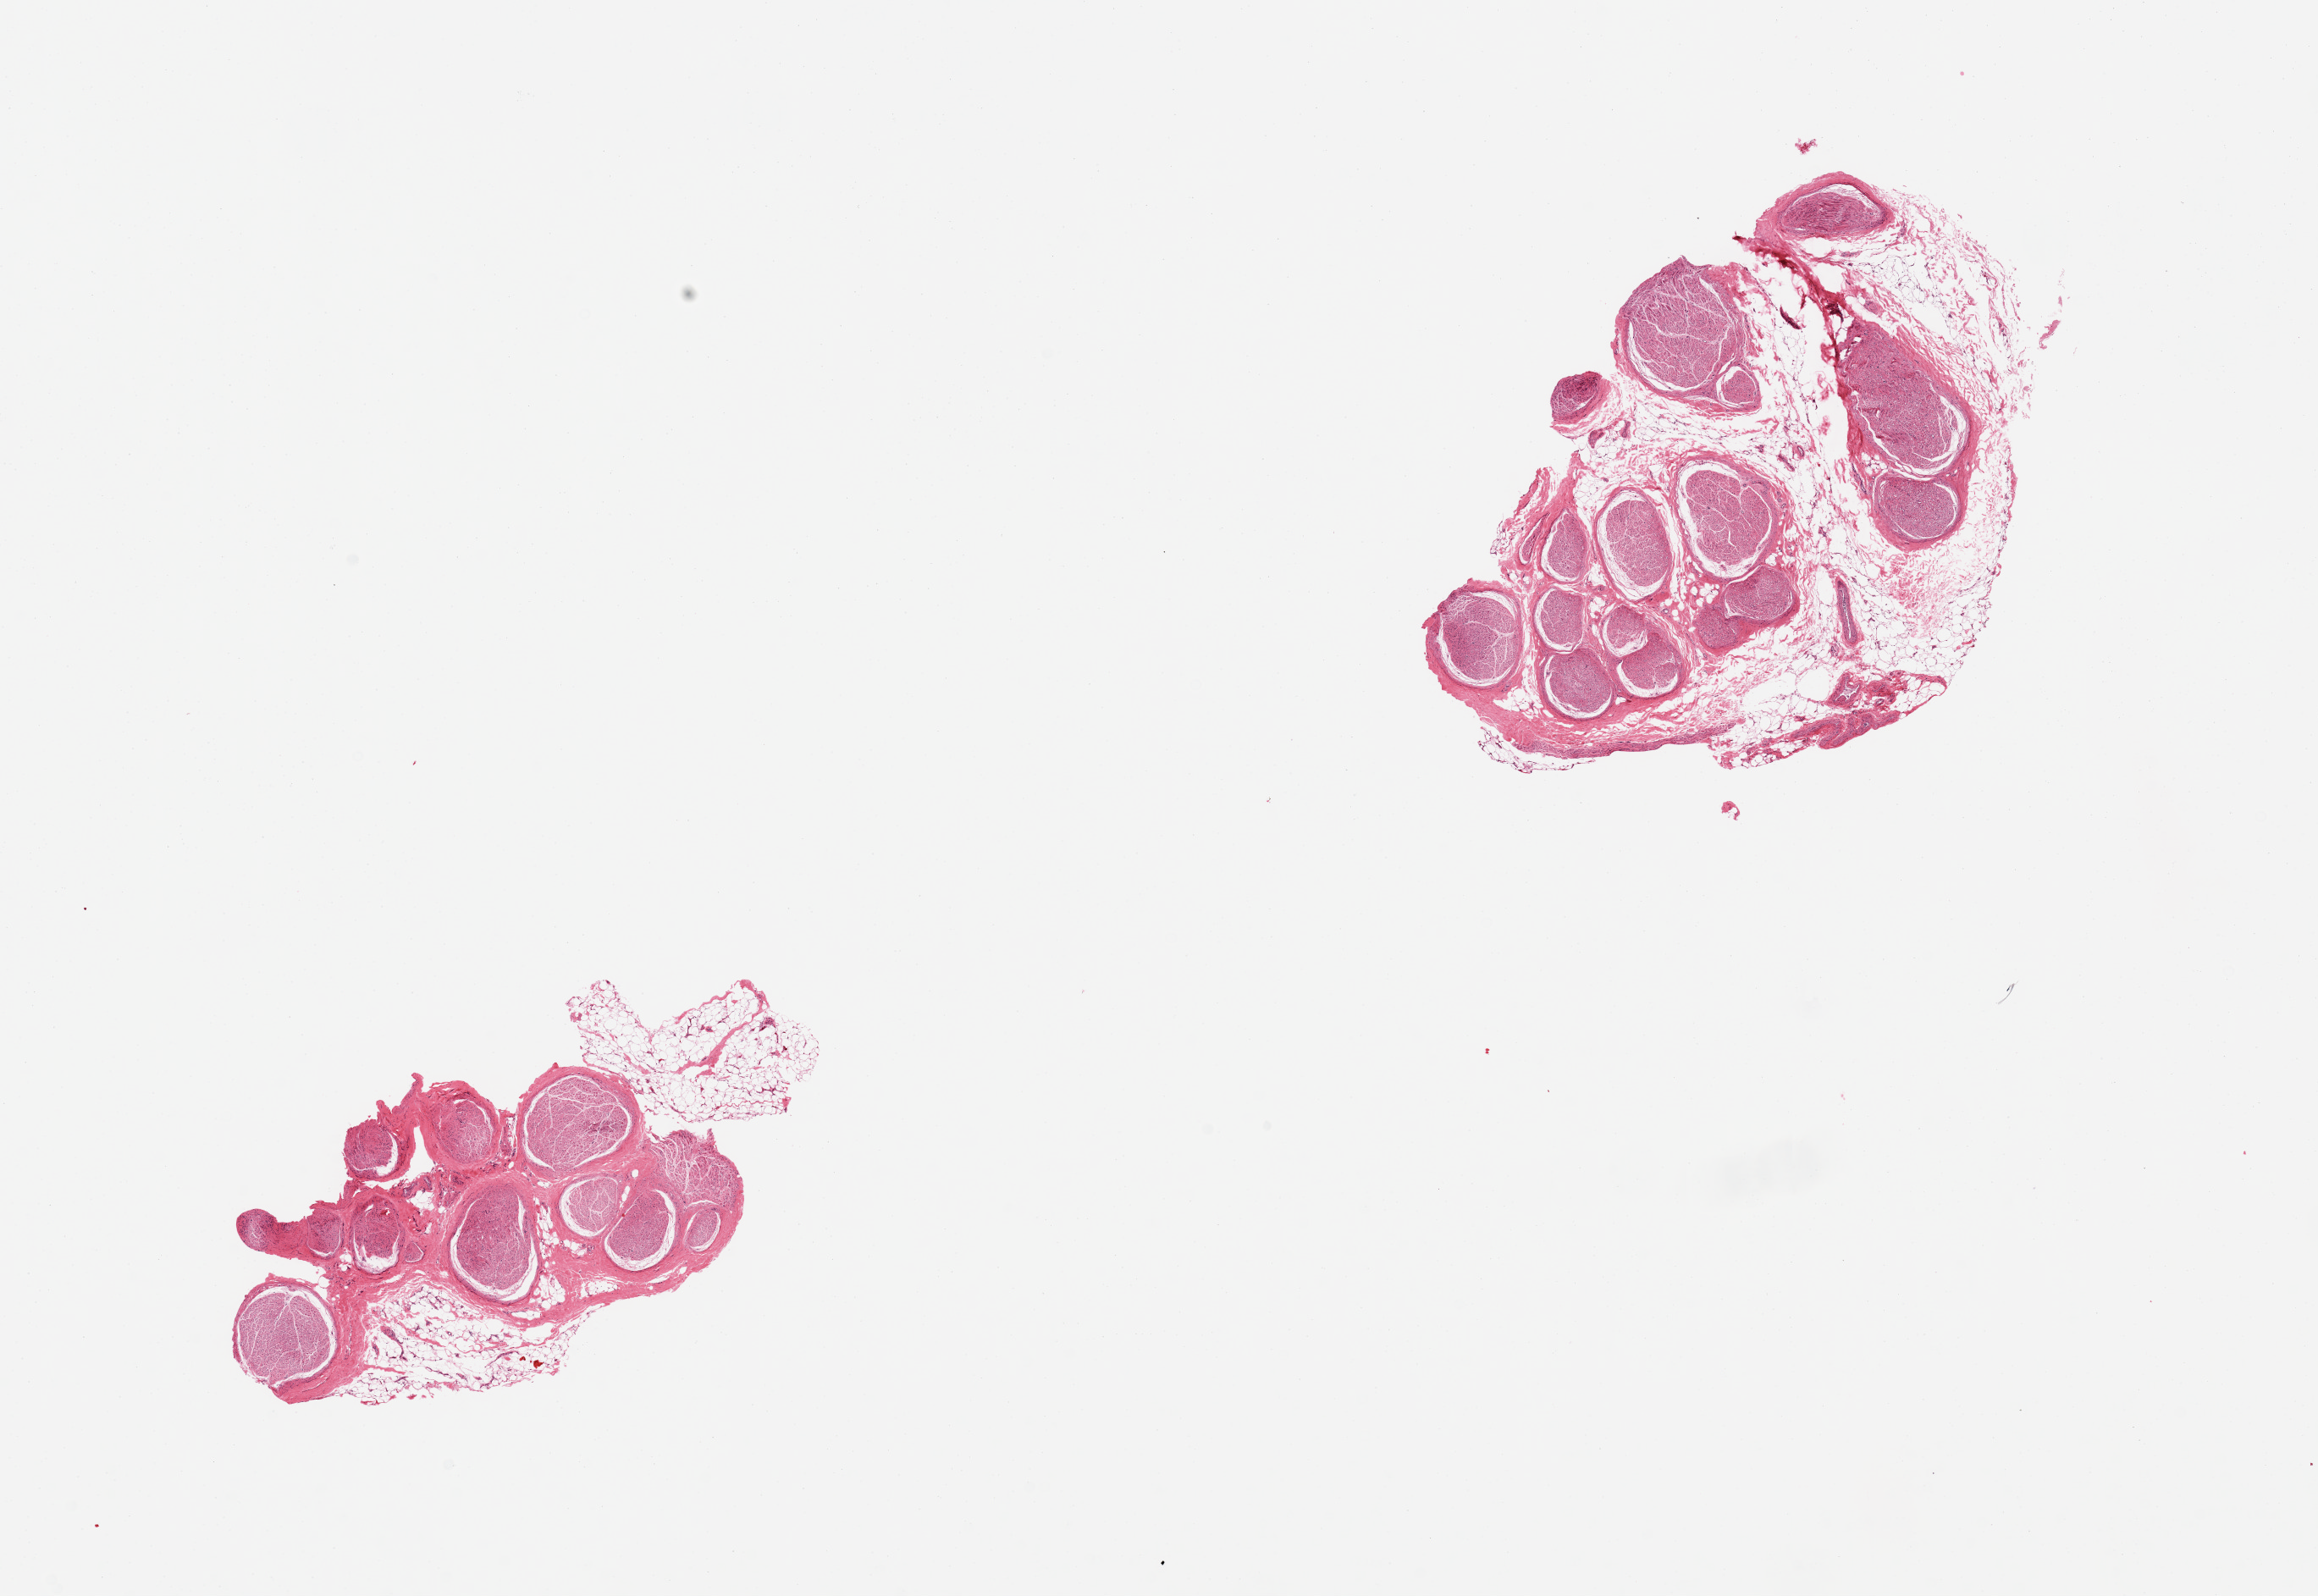
Hematoxylin and eosin (H&E) whole-slide image, brightfield, shown as a low-resolution overview of the whole scanned area (about 21.7 x 14.9 mm, from a 20x scan), PAXgene-fixed paraffin-embedded (PFPE) section, target tissue: tibial nerve, donor tissue sample. Donor: male.
Pathologist's review note for this sample: 2 pieces, adherent discontinuous rims of fat up to ~1mm.